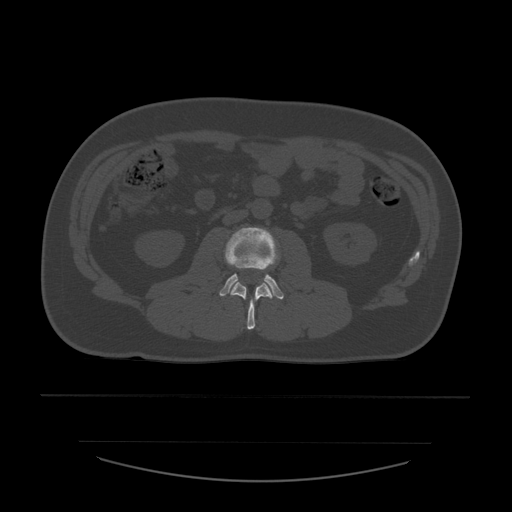
CT including the spine, one axial slice; position 186 of 532 along the scan axis; bone window (W 1800 / L 400 HU); 512 × 512 image matrix. Patient age 44 years. From the clinical record (not read from this slice): primary cancer: soft tissue sarcoma.
Structures marked on this image (semi-automatically segmented with operator editing):
- L2 vertebra: bounding box <231,282,273,330> (left, top, right, bottom; pixels)
- L3 vertebra: <220,227,284,300>